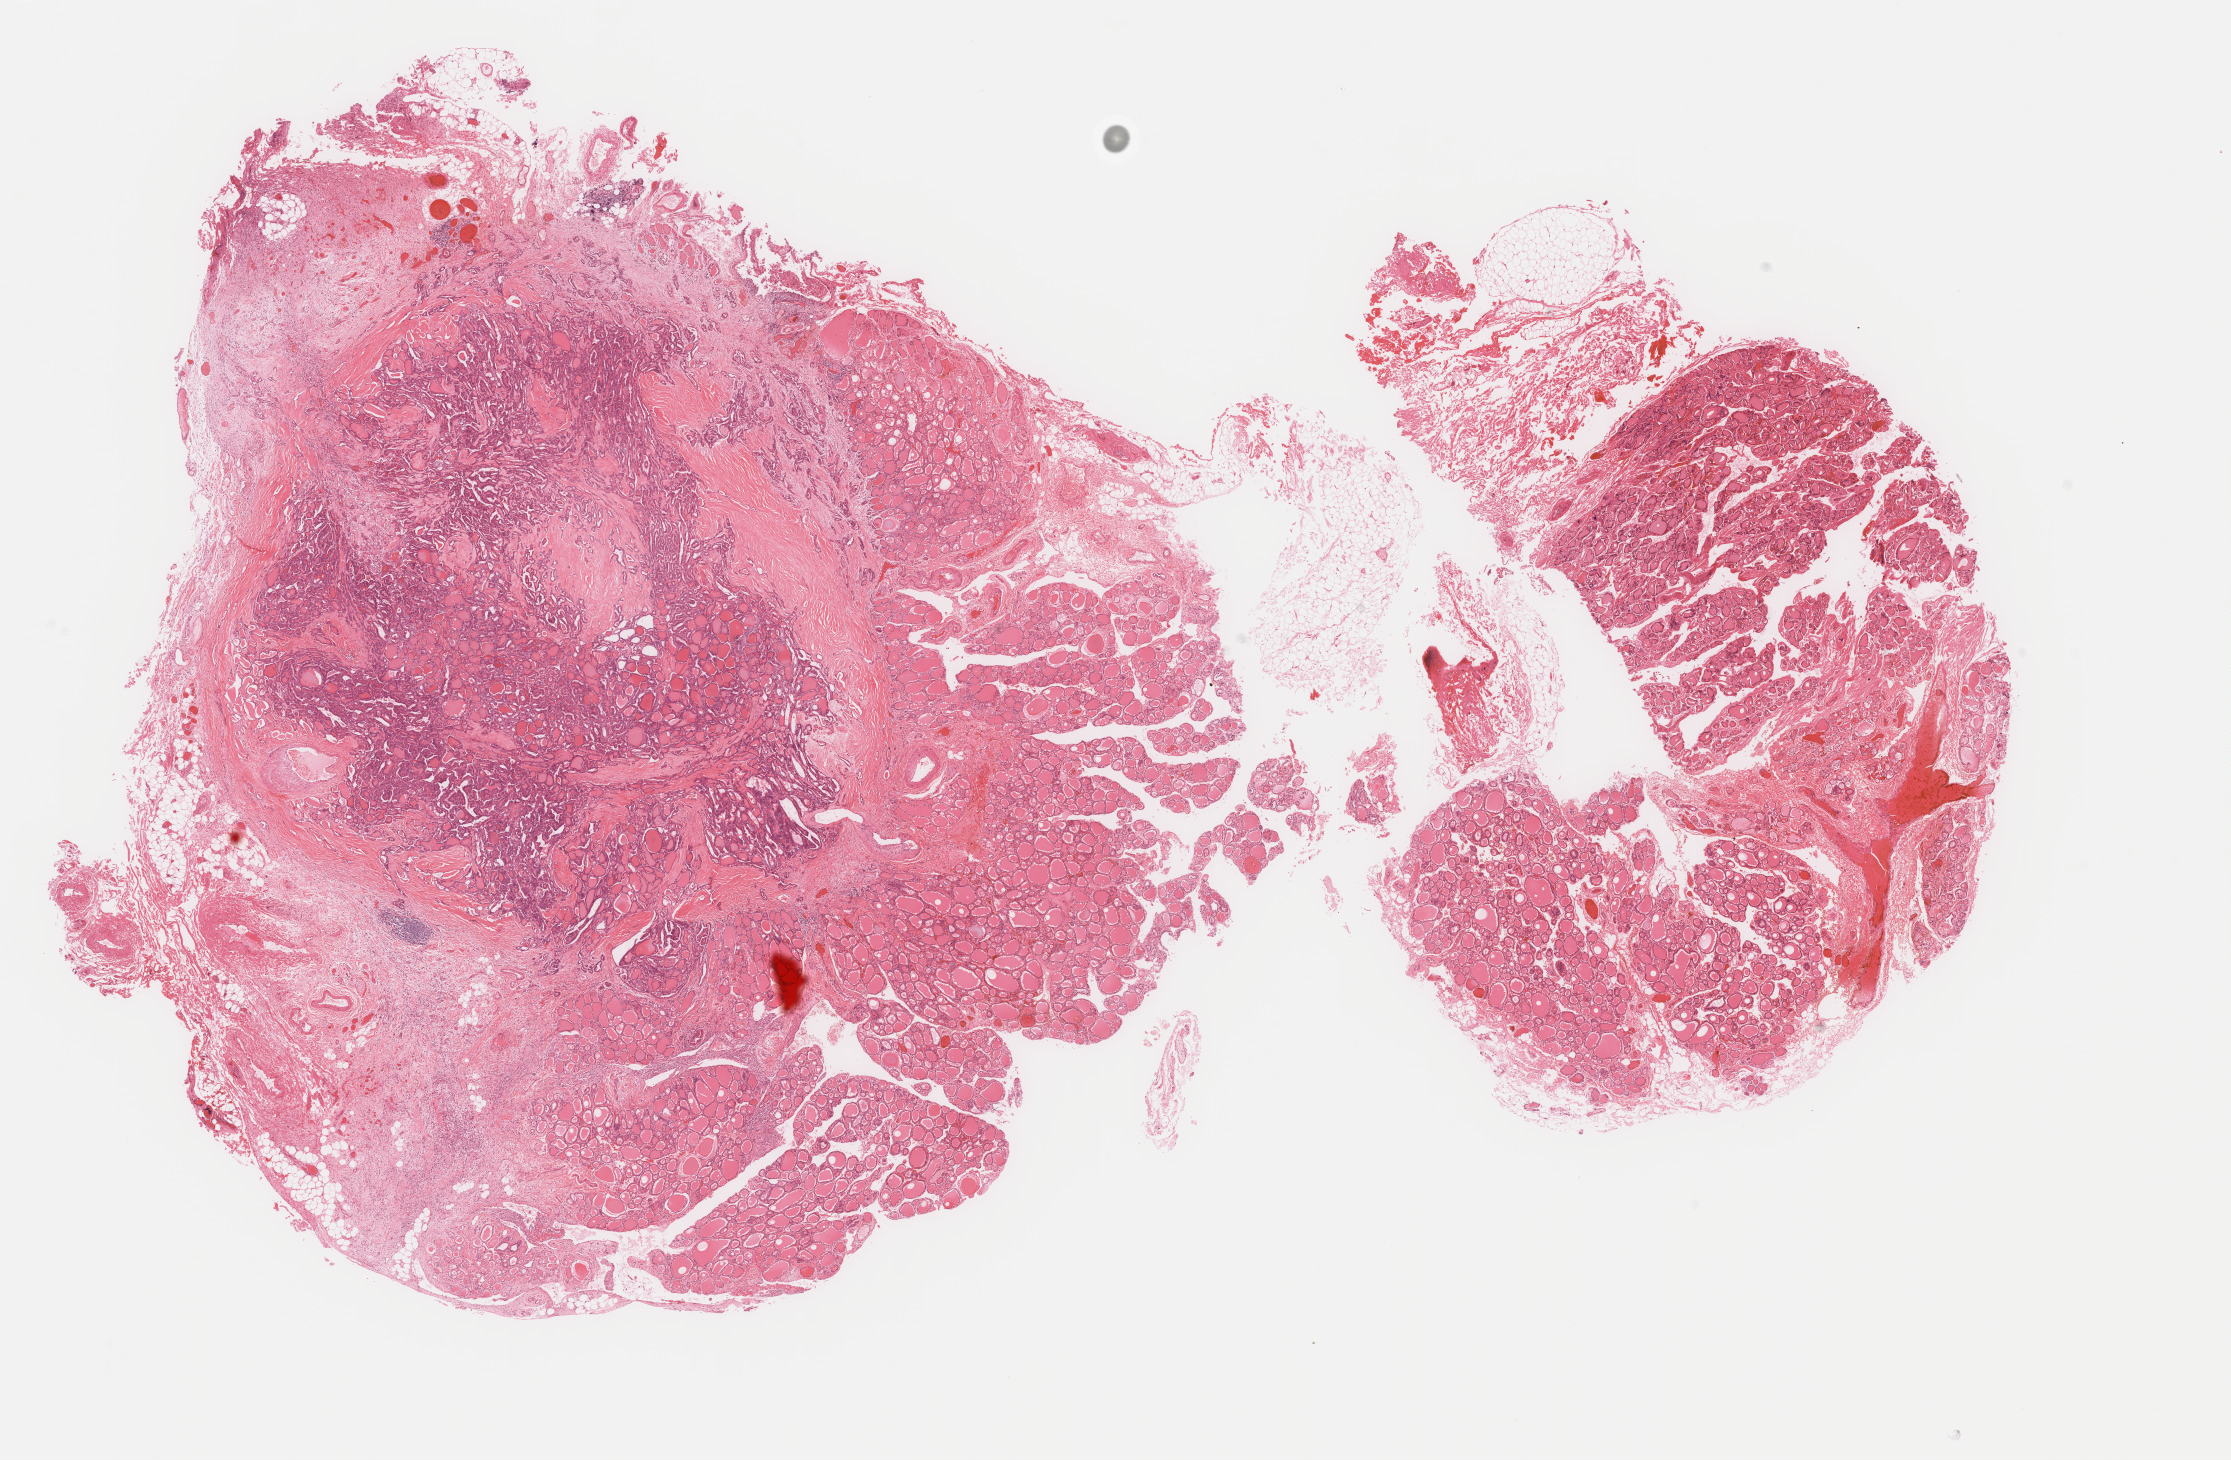
Digitized H&E-stained tissue section (whole slide) — low-resolution overview of the scanned area, about 17.7 x 11.6 mm (from a 40x scan). Formalin-fixed paraffin-embedded (FFPE) diagnostic section. Sample: primary tumour, thyroid. Patient: female, age at initial diagnosis 56 years.
AJCC pathologic stage: I. Histologic diagnosis: Papillary adenocarcinoma, NOS (thyroid gland).